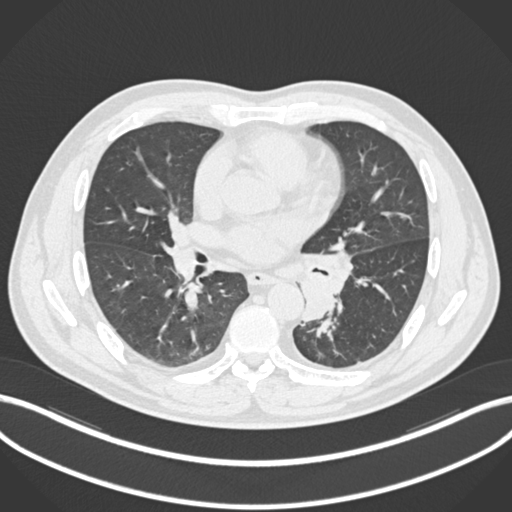
Chest CT, one axial slice; slice 113 of 223 in the series (ordered by position); lung window (W 1500 / L -600 HU); 512 × 512 image matrix, field of view 400 × 400 mm. Male patient, age 50 years. Case-level facts recorded for this patient, not image findings: clinical TNM (as recorded): T2a N3 M0.
Outlined on this slice (bounding box drawn by a radiologist):
- lung tumour (recorded histology: squamous cell carcinoma): bounding box <300,264,342,326> (left, top, right, bottom; pixels)